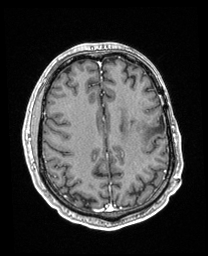
Brain MRI from a brain-tumour surgery series, one axial slice. Position 80 of 208 along the scan axis. T1-weighted post-contrast. 208 × 256 image matrix, field of view 211 × 260 mm. Case-level facts recorded for this patient, not image findings: histopathology: Astrocytoma; WHO grade: 3; IDH mutation: yes.
Annotated regions visible in this slice (expert manual segmentation):
- previous resection cavity: bounding box <156,116,165,132> (left, top, right, bottom; pixels)